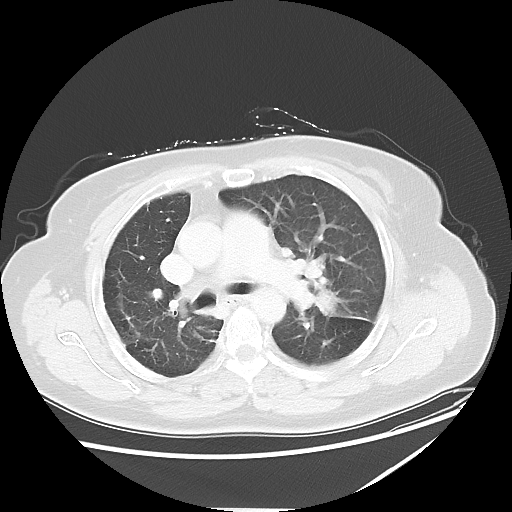
Chest CT, one axial slice. Position 36 of 54 along the scan axis. Lung window (W 1500 / L -600 HU). 5 mm slice thickness. 512 × 512 image matrix, field of view 384 × 384 mm. Patient: female, 61 years. From the clinical record (not read from this slice): clinical TNM (as recorded): T1c N3 M1.
Annotated regions visible in this slice (rectangle marked by the reading radiologist):
- lung tumour (recorded histology: adenocarcinoma): box from (x=314, y=285) to (x=373, y=327) px